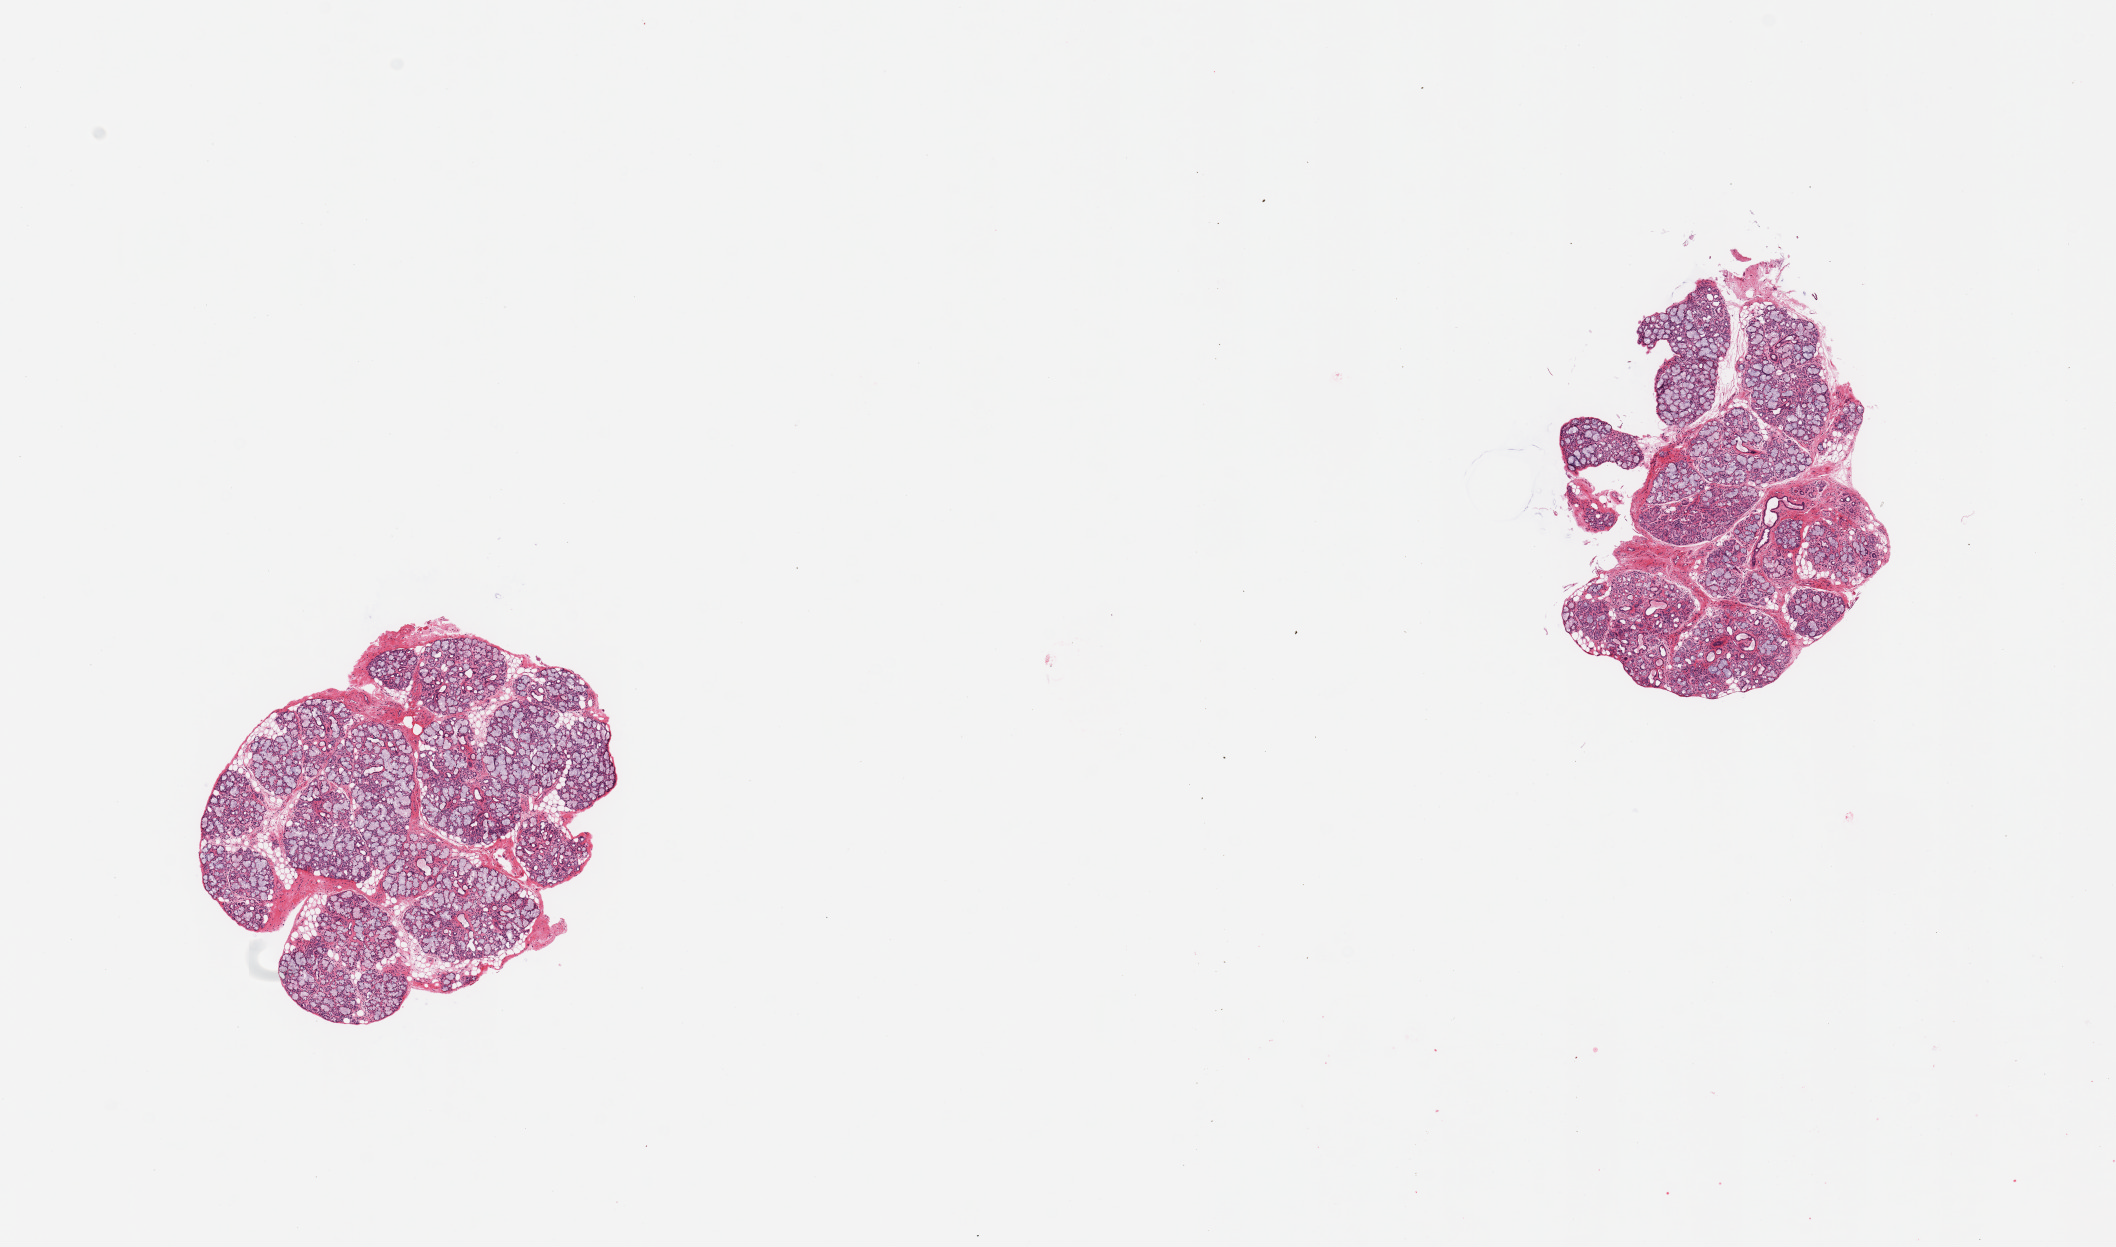
Hematoxylin and eosin (H&E) whole-slide image — whole scanned area (about 16.7 x 9.9 mm) shown as a low-resolution overview; PAXgene-fixed, paraffin-embedded tissue; sampled site (target tissue): minor salivary gland; tissue donor sample.
Review note (as recorded): 2 pieces; well trimmed, salivary gland elements with small component of internal fat.